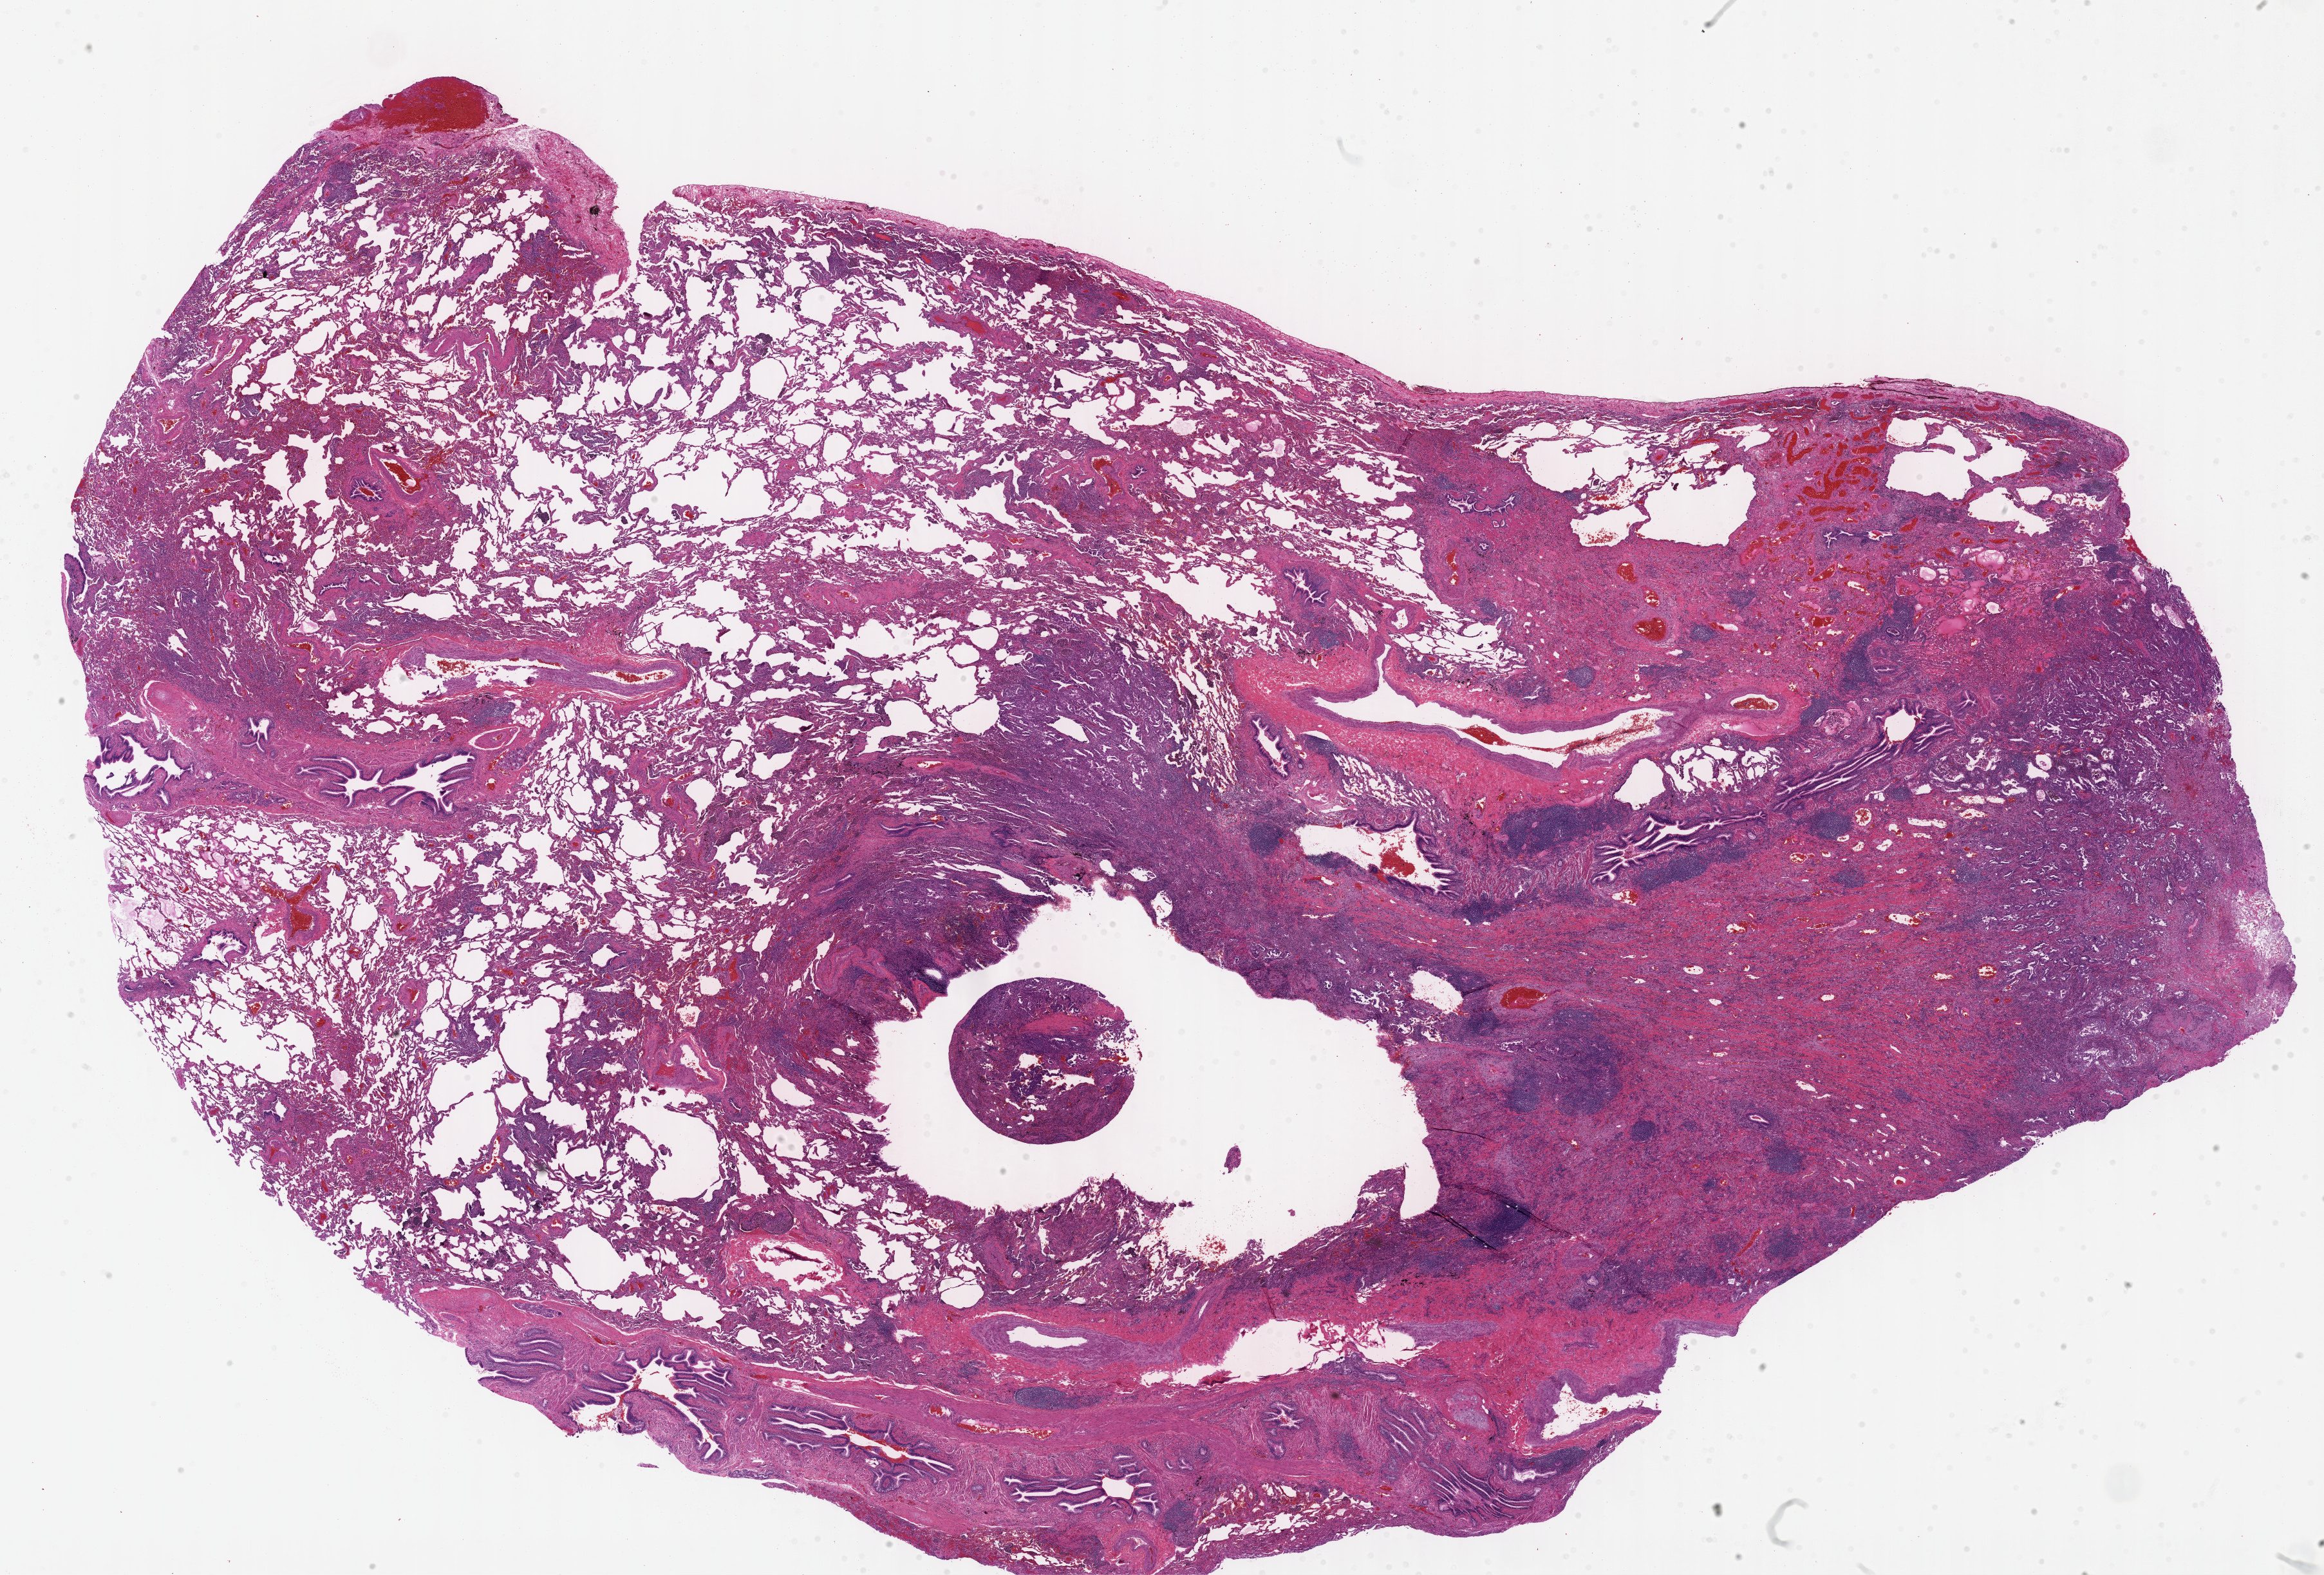
Whole-slide histology image, Hematoxylin and eosin (H&E) stained — shown as a low-resolution overview of the whole scanned area (about 29.2 x 19.8 mm, slide scanned at 40x); formalin-fixed paraffin-embedded (FFPE) diagnostic section; primary tumour sample from the lung. Female, age 56 years at initial diagnosis.
Diagnosis: Adenocarcinoma, NOS (lower lobe, lung).